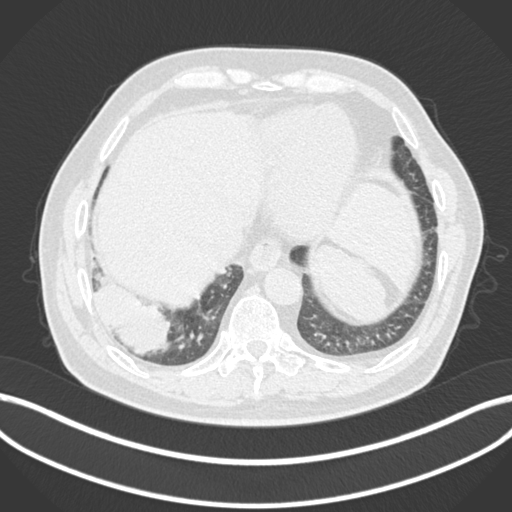
Chest CT, one axial slice; 120 kVp; lung window (W 1500 / L -600 HU); 1 mm slice thickness; 512 × 512 image matrix, field of view 400 × 400 mm. Patient: male, 59 years.
Annotated regions visible in this slice (rectangle marked by the reading radiologist):
- lung tumour (recorded histology: adenocarcinoma): box from (x=90, y=277) to (x=173, y=358) px